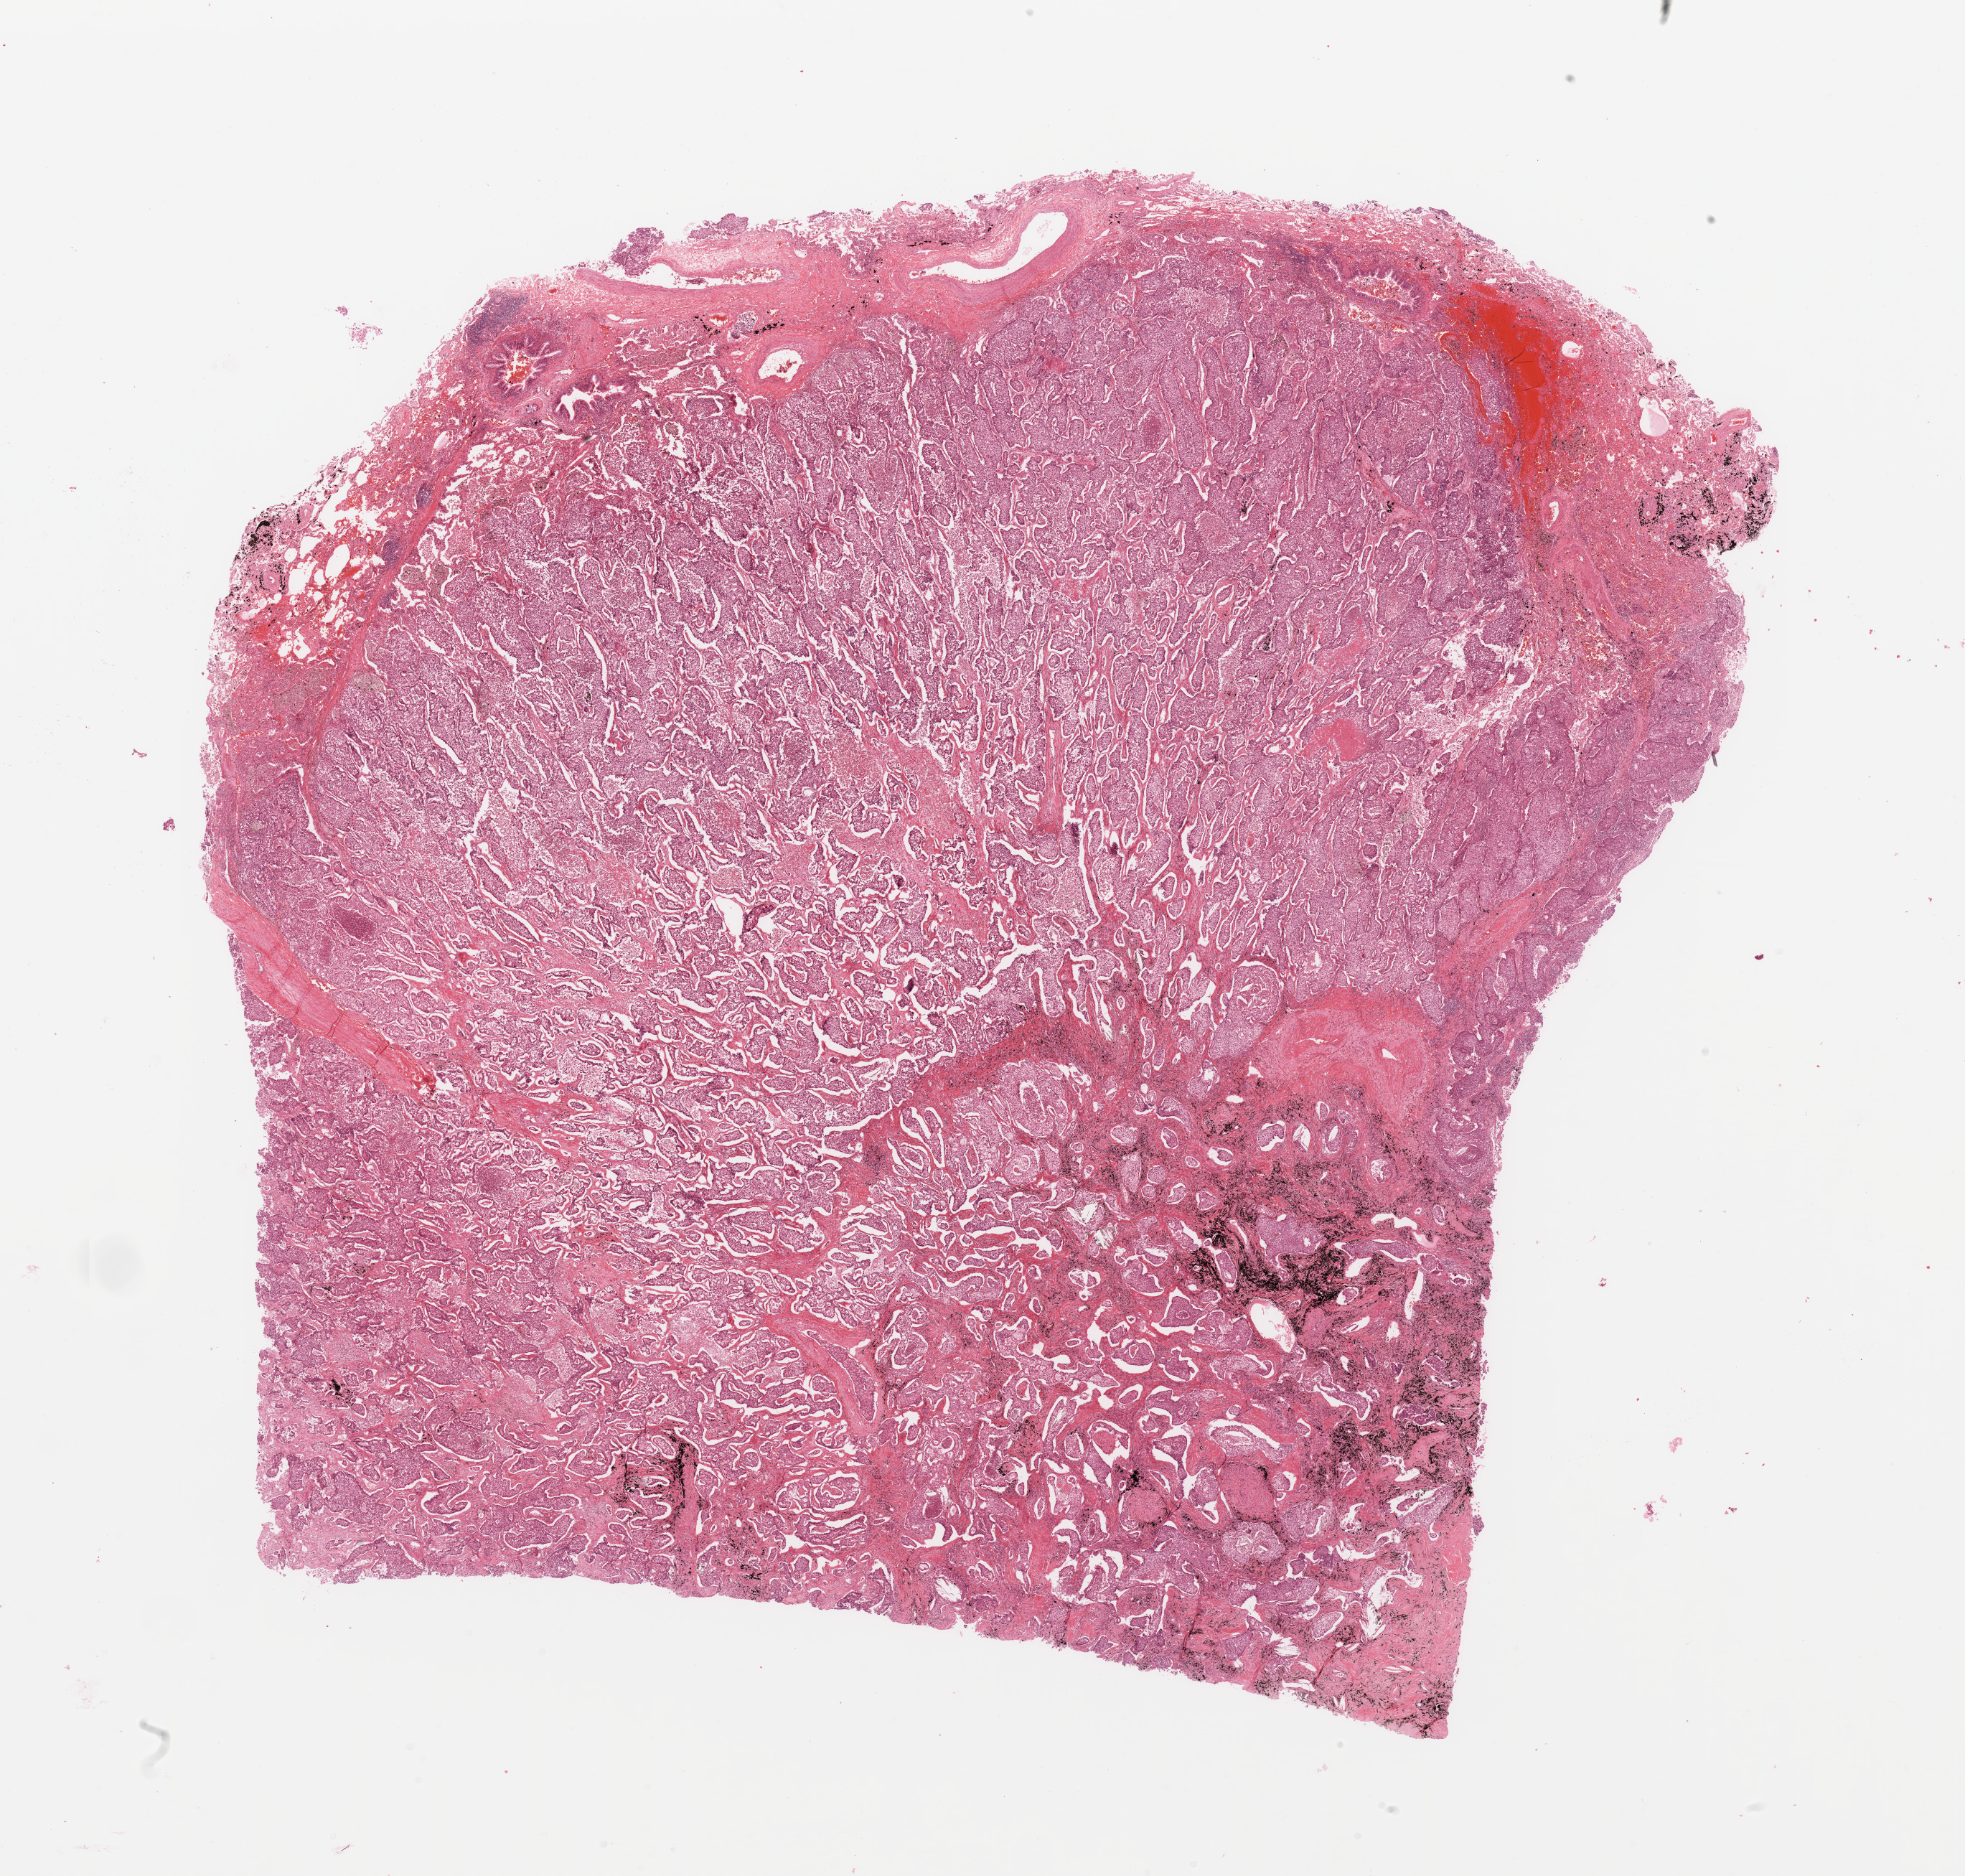
Whole-slide histology image, Hematoxylin and eosin (H&E) stained, whole scanned area (about 21.7 x 20.7 mm, slide scanned at 20x) shown as a low-resolution overview. Tumour tissue sample, lung. Patient: male, age 64 years. Histologic grade: G3 (poorly differentiated).
• AJCC pathologic stage: IIB
• diagnosis: Adenocarcinoma, NOS